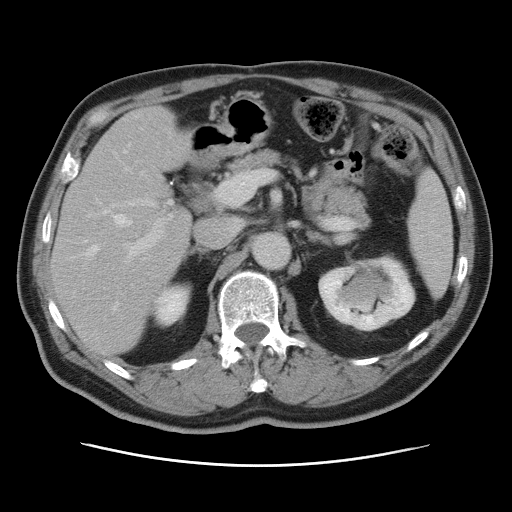
Contrast-enhanced abdominal CT, one axial slice; slice 43 of 80 in the series (ordered by position); 120 kVp; intravenous contrast given; soft-tissue window (W 400 / L 40 HU); 5 mm slice thickness; 512 × 512 image matrix. Male patient, age 69 years. From the clinical record (not read from this slice): diagnosis: colorectal cancer liver metastases, imaged before liver resection; multiple liver metastases: no; largest metastasis: 5 cm.
Annotated regions visible in this slice (expert manual segmentation):
- hepatic veins: bounding box <84,151,131,311> (left, top, right, bottom; pixels)
- liver: <53,109,190,354>
- planned liver remnant (the part of the liver to remain after resection): <53,187,190,354>
- portal vein (with intrahepatic branches): <125,168,172,263>